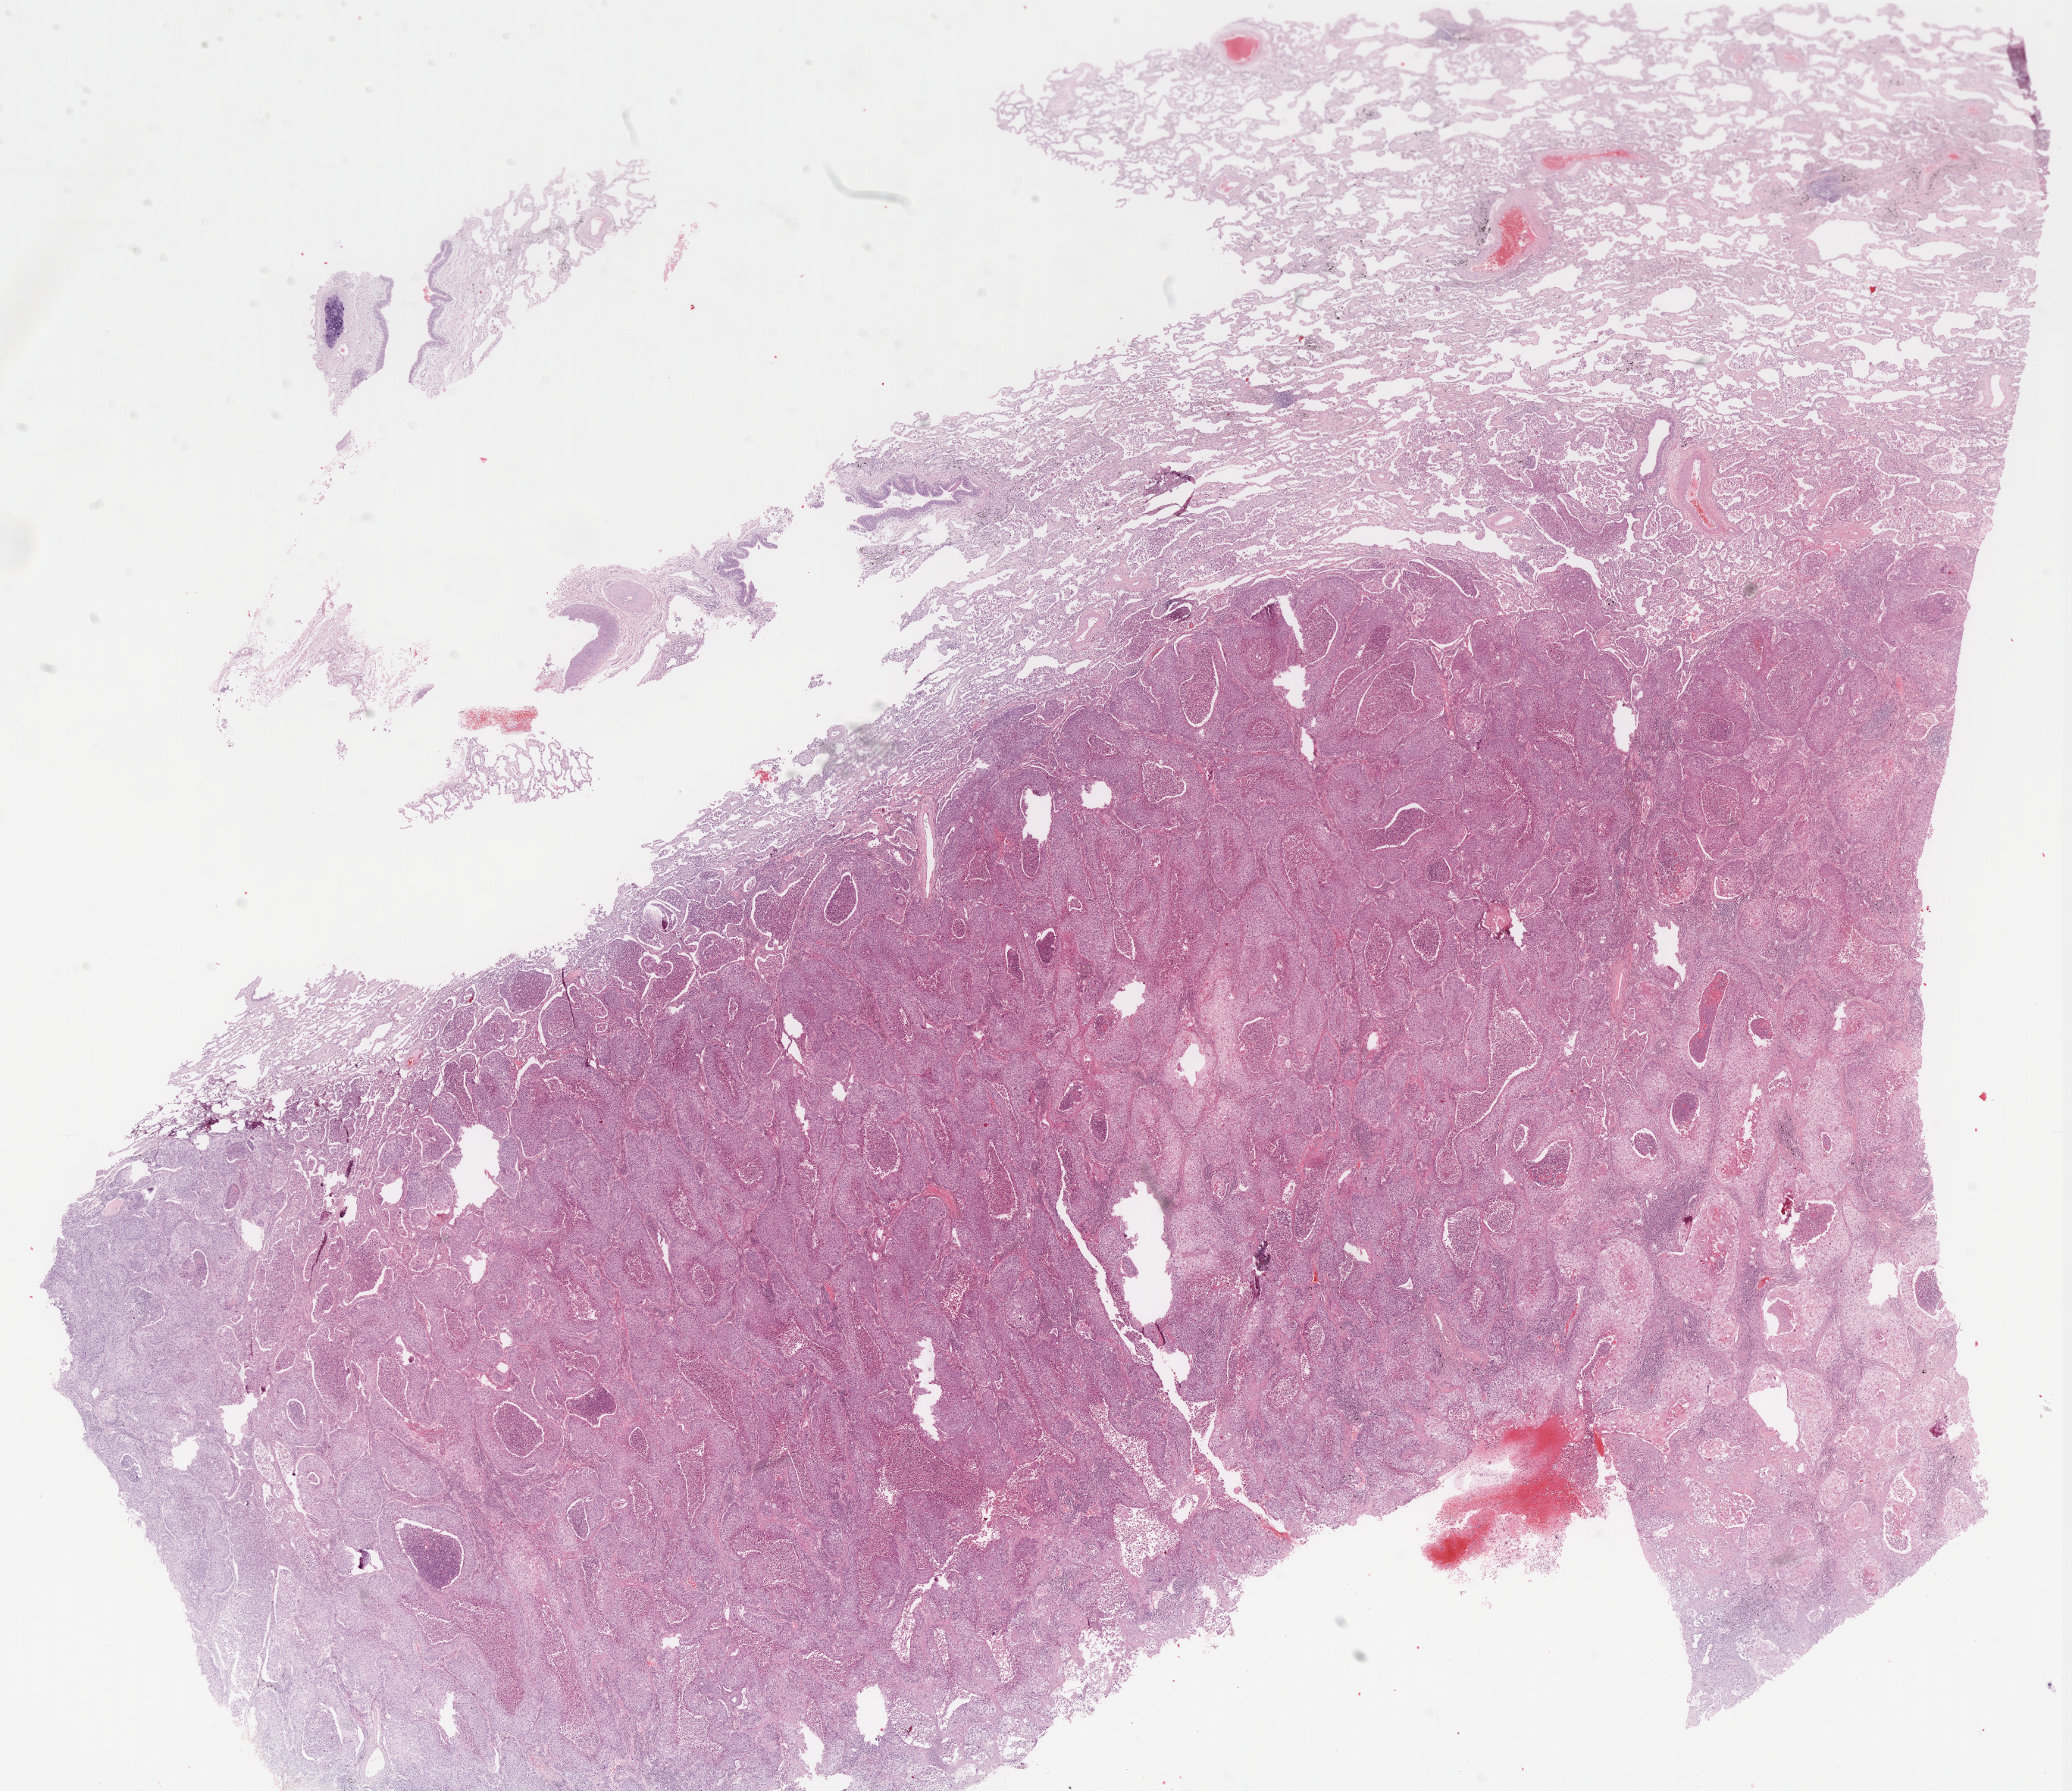
H&E whole-slide image, whole scanned area (about 22.0 x 19.0 mm, from a 40x scan) shown as a low-resolution overview, formalin-fixed paraffin-embedded (FFPE) diagnostic section, sample: primary tumour, lung. Male patient; age at initial diagnosis 64 years.
Diagnosis: Squamous cell carcinoma, NOS (lower lobe, lung). AJCC pathologic stage: IIB. Laterality: right.